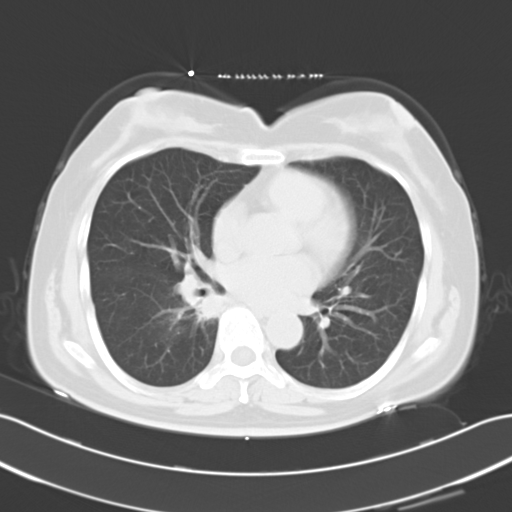
Chest CT, one axial slice. Slice 14 of 27 in the series (ordered by position). Lung window (W 1500 / L -600 HU). 10 mm slice thickness. 512 × 512 image matrix, field of view 353 × 353 mm. Patient: female, 59 years. From the clinical record (not read from this slice): clinical TNM (as recorded): T1c N0 M1b.
Annotated regions visible in this slice (rectangle marked by the reading radiologist):
- lung tumour (recorded histology: adenocarcinoma): bounding box (x1, y1, x2, y2) in pixels: (189, 289, 226, 325)